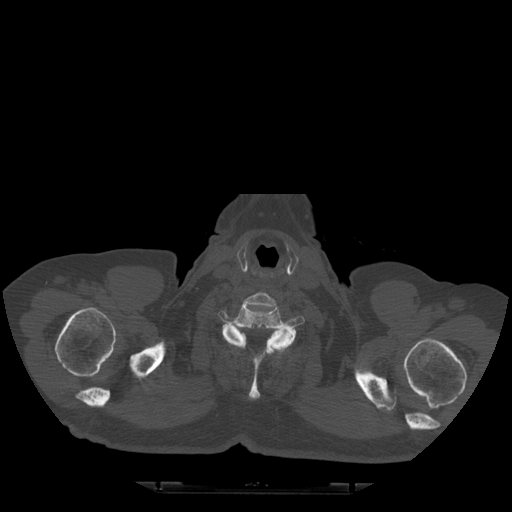
CT including the spine, one axial slice; slice 450 of 522 in the series (ordered by position); bone window (W 1800 / L 400 HU); 512 × 512 image matrix, field of view 420 × 420 mm. Patient age 72 years. Case-level facts recorded for this patient, not image findings: primary cancer: prostate.
Outlined on this slice (semi-automatically segmented with operator editing):
- T1 vertebra: bounding box (x1, y1, x2, y2) in pixels: (213, 326, 304, 400)